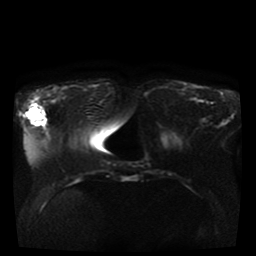
Breast MRI, one axial slice. Position 15 of 41 along the scan axis. Diffusion-weighted series; image 2 of 4 stored at this slice position (different b-values; order by instance number). 1.5 T. 256 × 256 image matrix, field of view 330 × 330 mm. Female patient.
Structures marked on this image (manually delineated by an expert):
- tumour on diffusion-weighted imaging: bounding box [x1, y1, x2, y2] px = [30, 108, 44, 123]